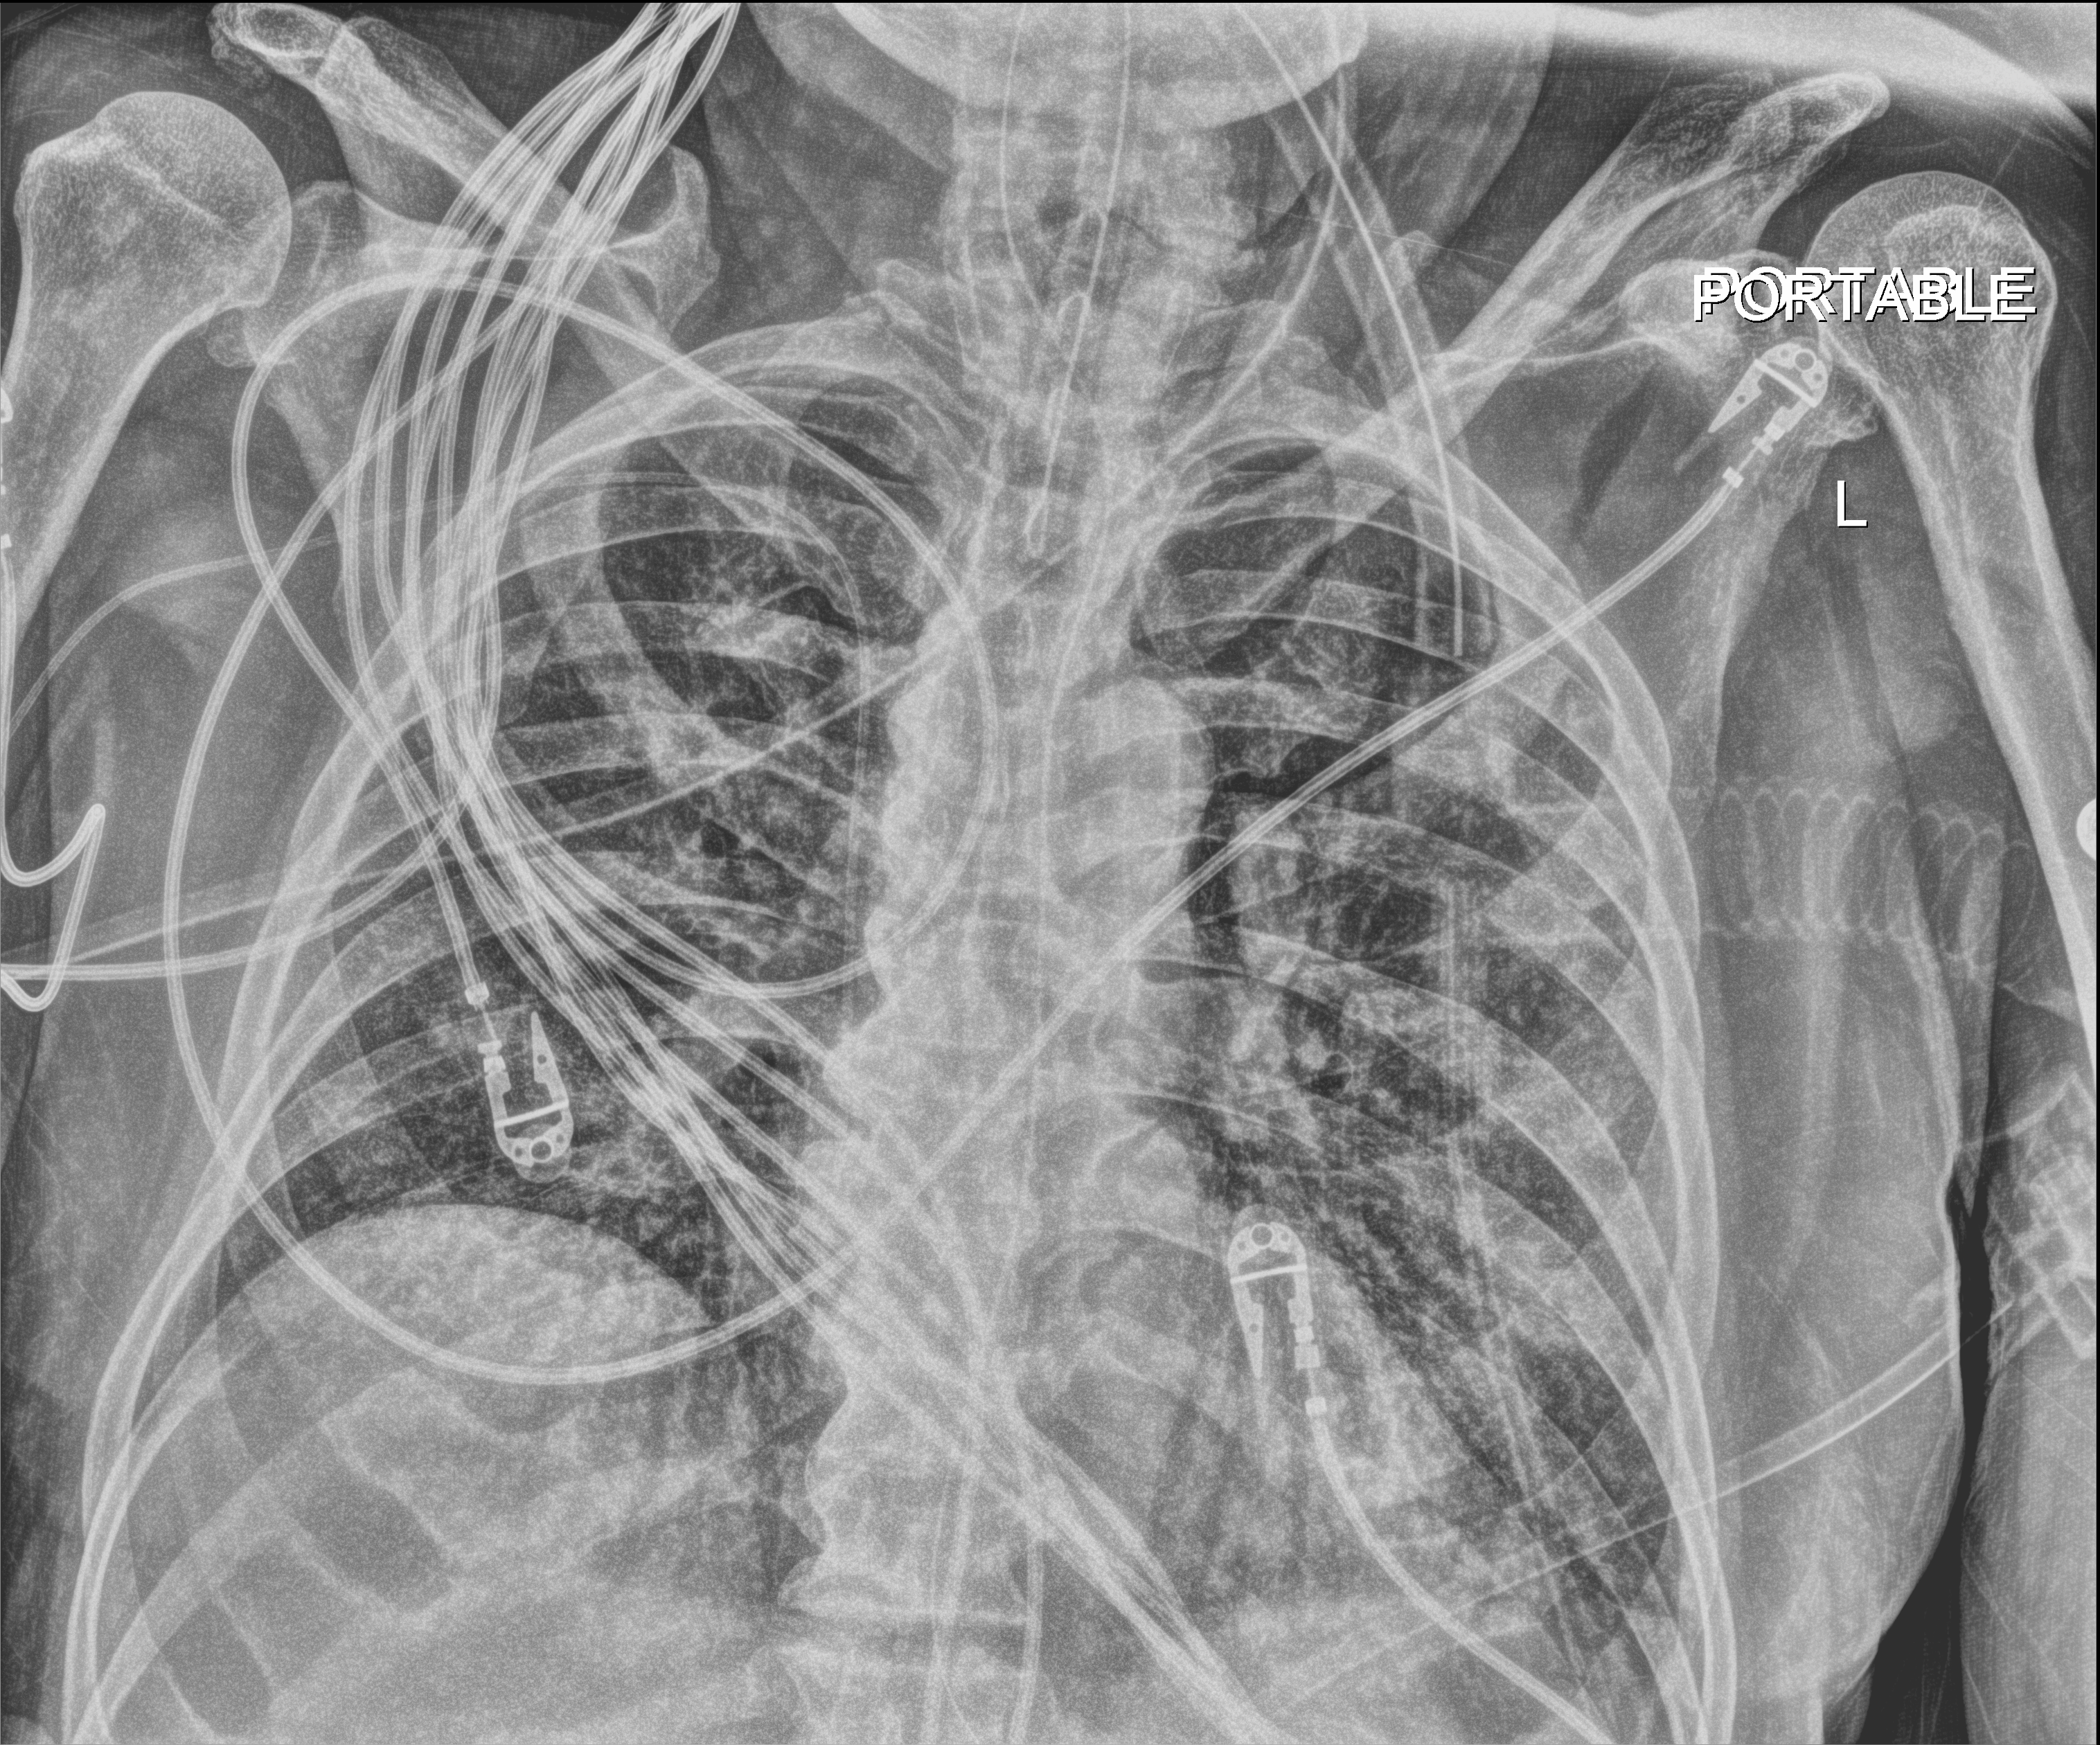
Chest X-ray (portable); anteroposterior (AP) projection. Patient hospitalised with COVID-19; male, aged 75–90 years.
Admission-level facts for this patient (not findings on this image; timing relative to this image not recorded): COPD (admission record): no; length of hospital stay: 33 days.